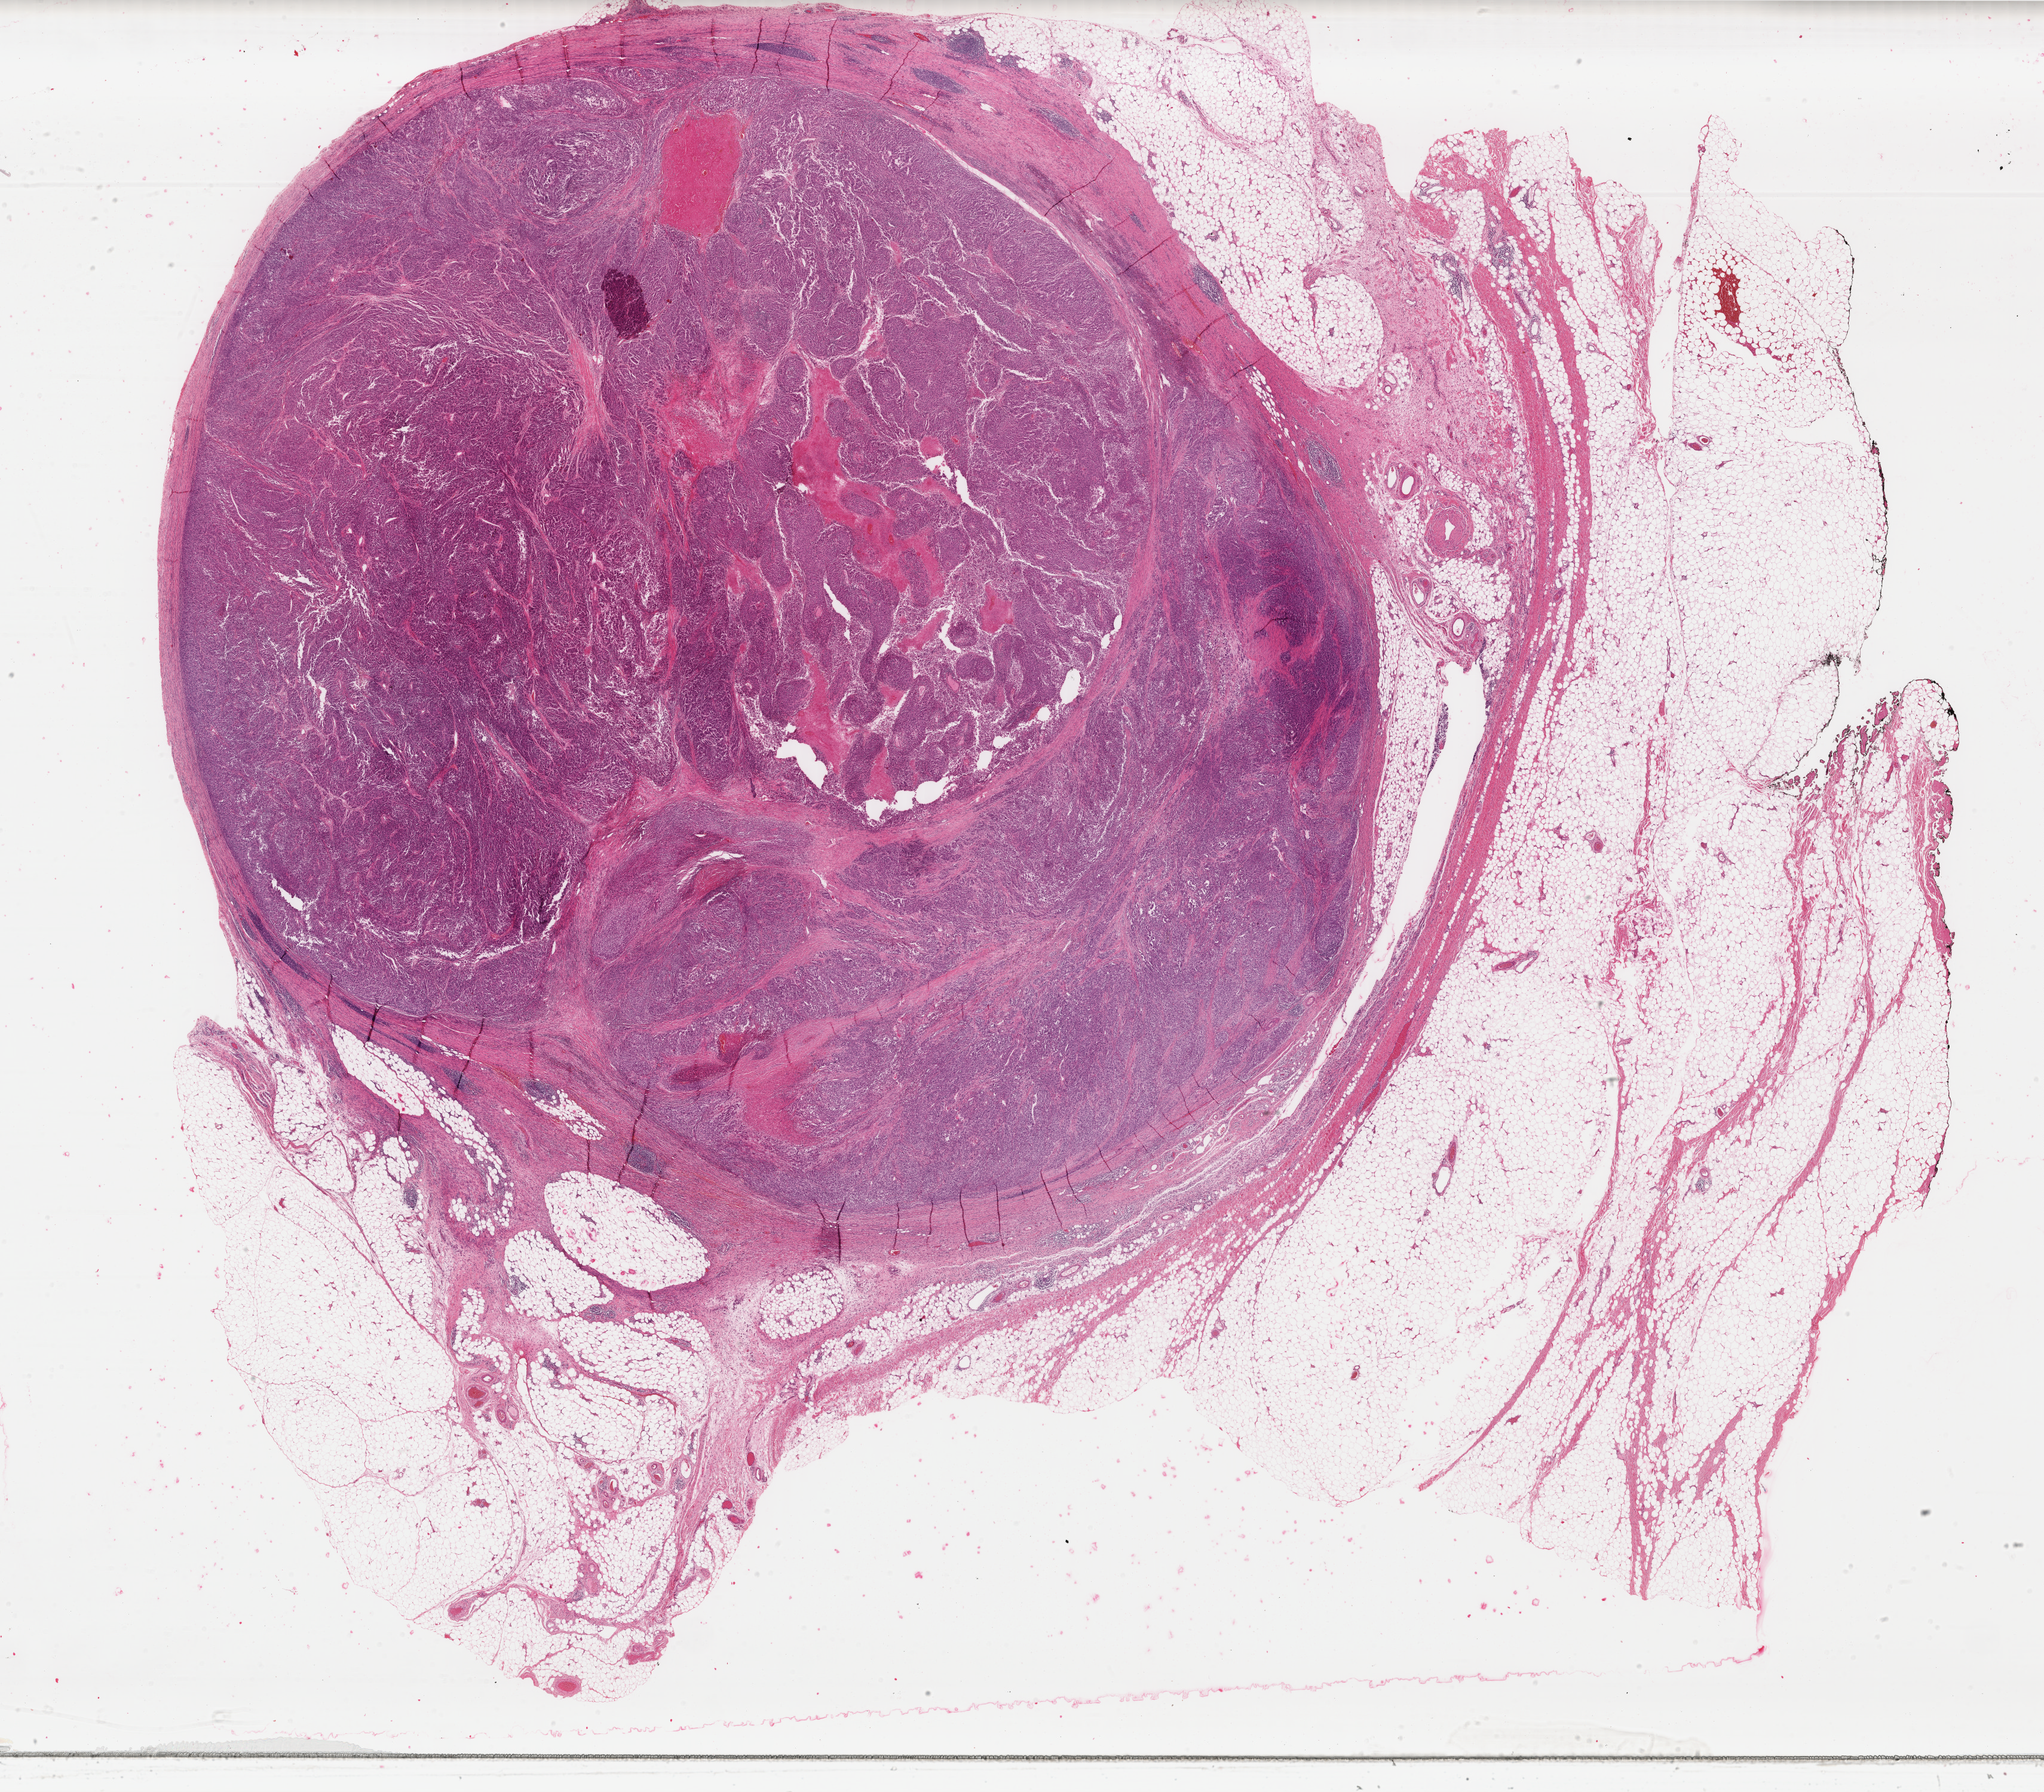
H&E-stained whole-slide image — whole scanned area (about 27.2 x 23.8 mm, slide scanned at 40x) shown as a low-resolution overview; formalin-fixed paraffin-embedded (FFPE) diagnostic section; skin, primary tumour sample. Patient: male, age at initial diagnosis 34 years.
Diagnosis: Malignant melanoma, NOS.